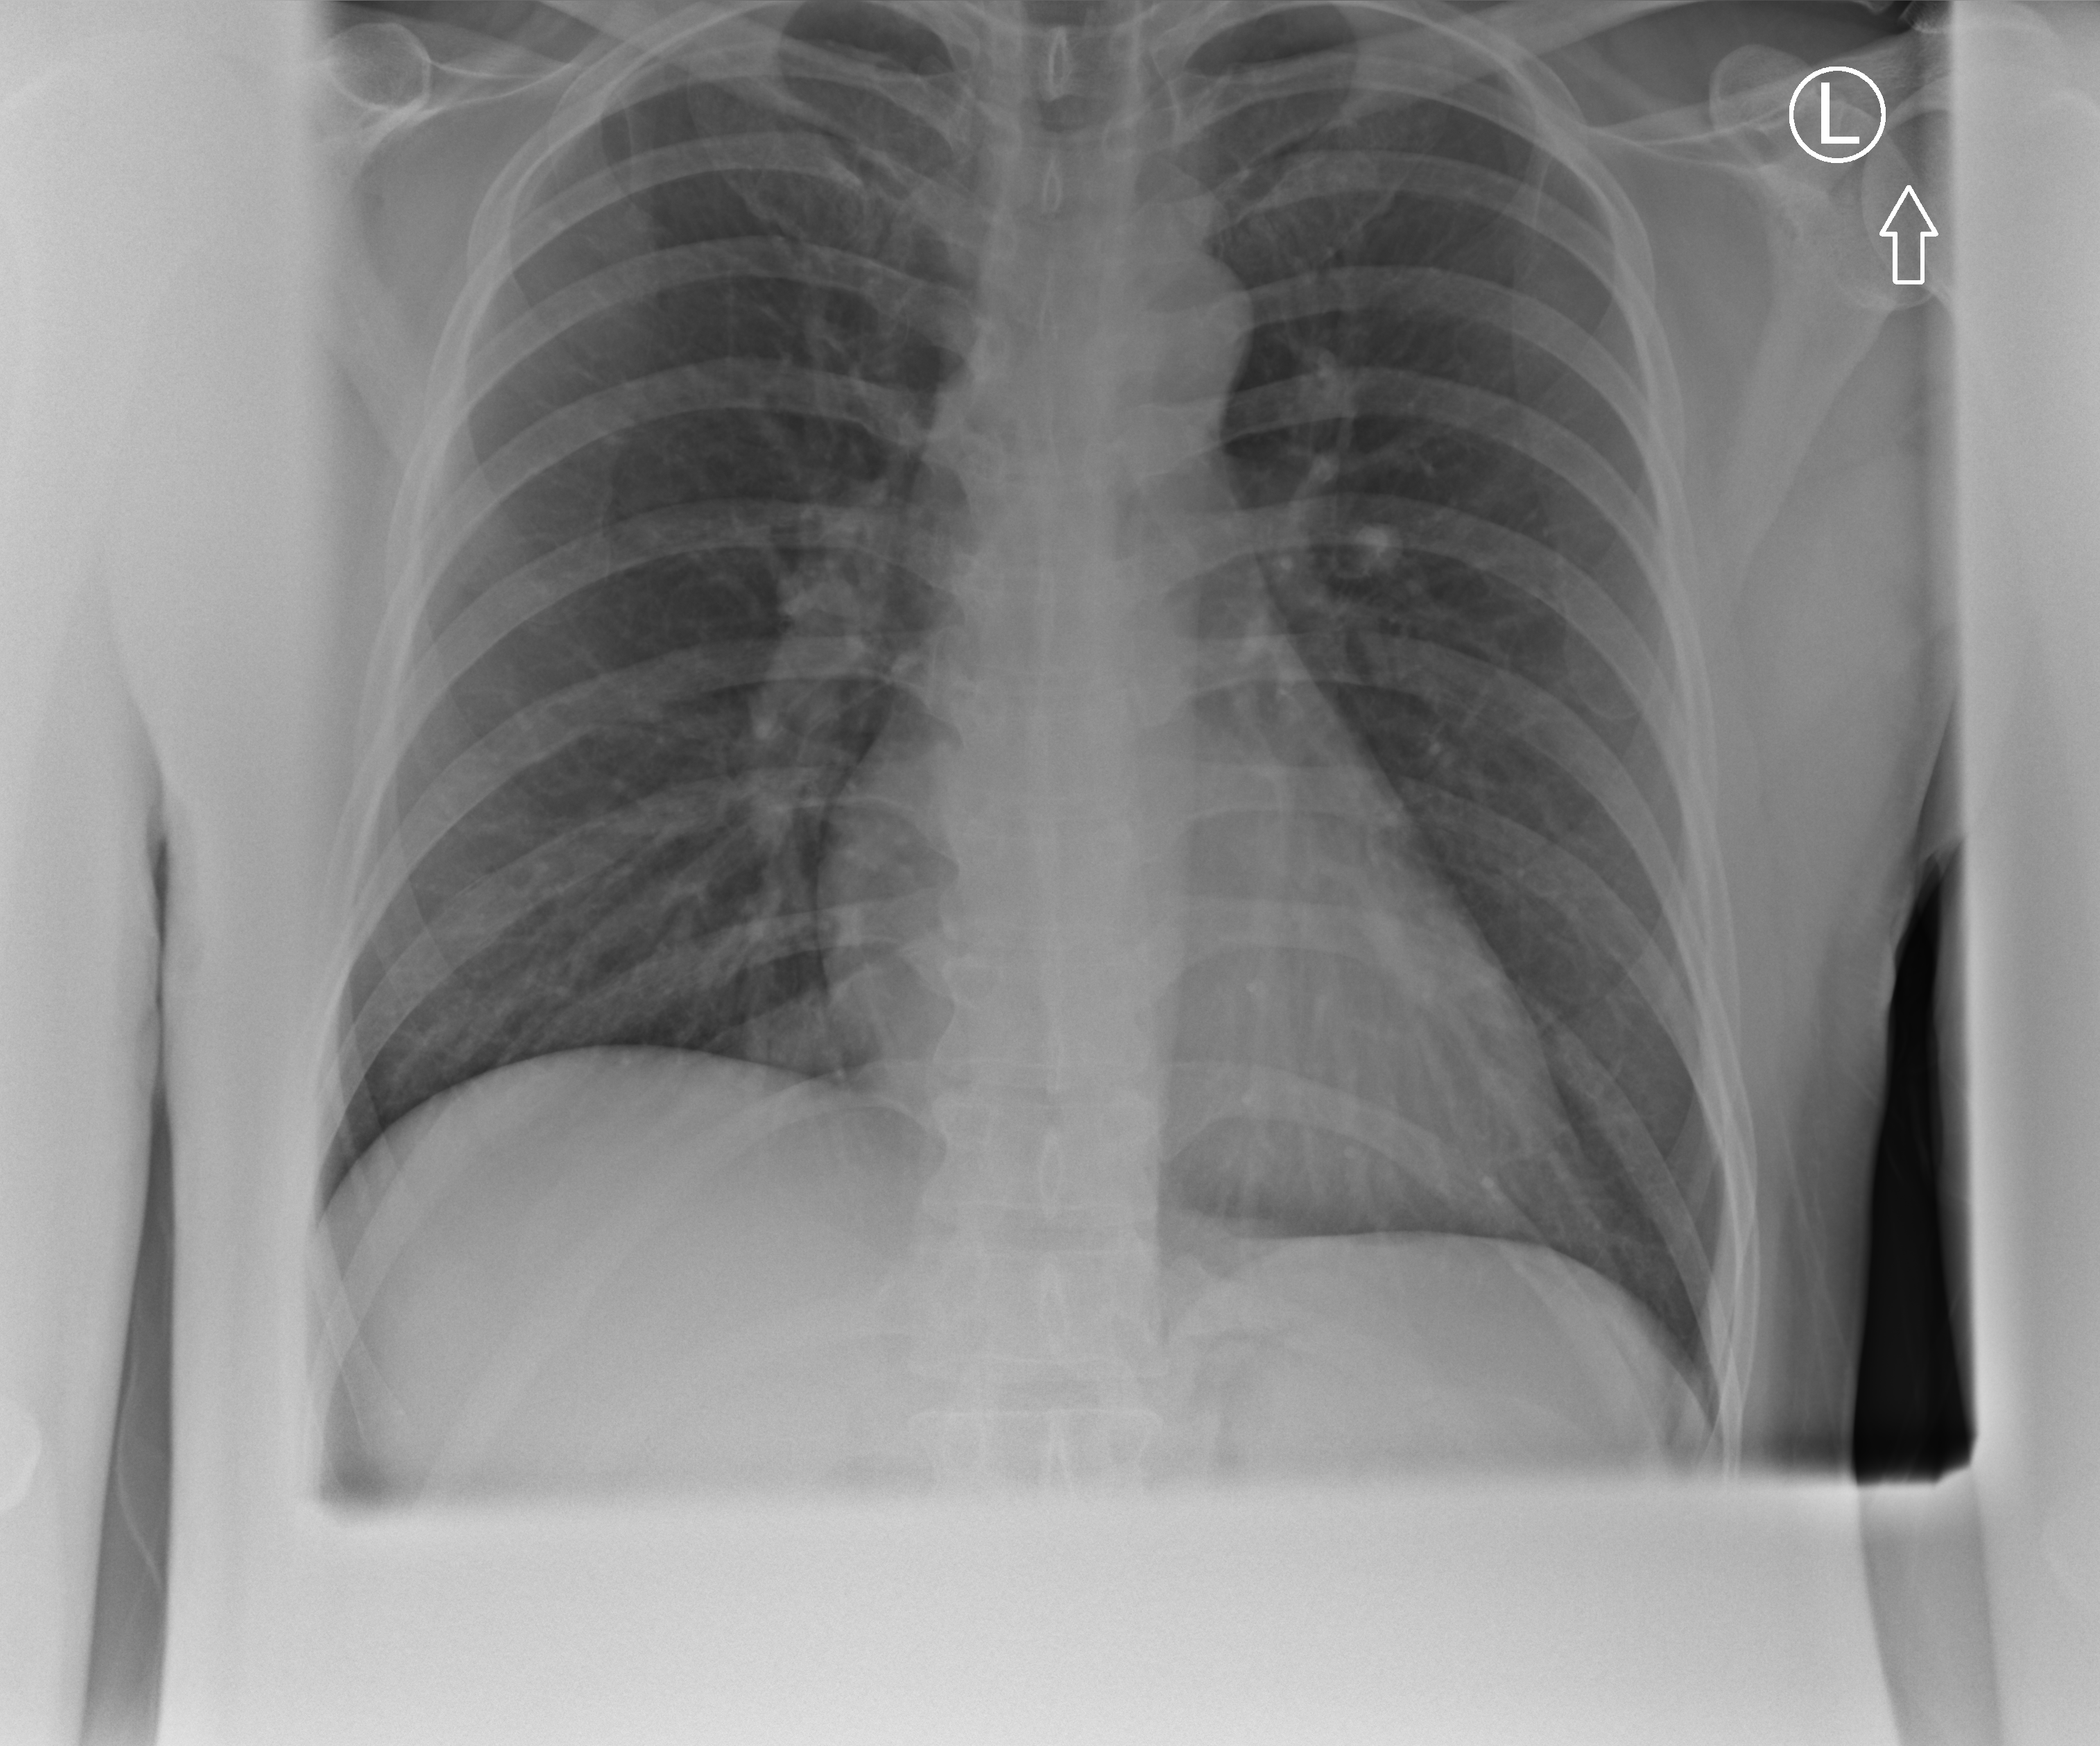
Chest X-ray (portable). Patient hospitalised with COVID-19; male, aged 18–59 years.
Hospital-stay facts (about this admission, not read from this image; timing relative to this image not recorded):
- mechanically ventilated during this hospital stay: no
- admitted to intensive care during this hospital stay: no
- length of hospital stay: 1 day